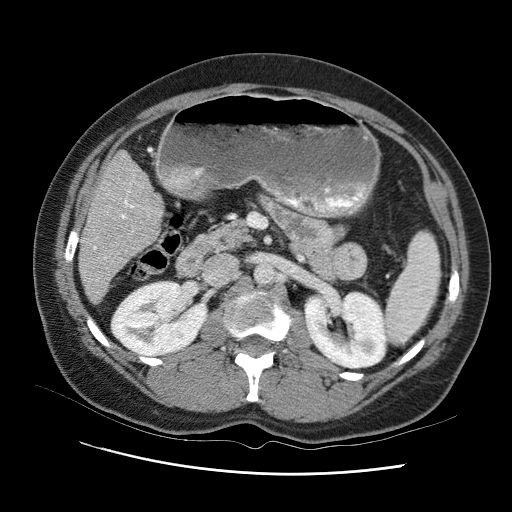
Contrast-enhanced abdominal CT (liver protocol), one axial slice. Position 36 of 95 along the scan axis. 120 kVp. One of 2 acquisitions stored at this slice position. Soft-tissue window (W 400 / L 40 HU). 512 × 512 image matrix, field of view 360 × 360 mm. Case-level facts recorded for this patient, not image findings: diagnosis: hepatocellular carcinoma (patient treated with transarterial chemoembolisation; whether this scan precedes or follows treatment is not stated here); TNM stage (as recorded): Stage-I; Child-Pugh class: B.
Structures marked on this image (semi-automatically segmented with operator editing):
- liver parenchyma outside the tumour (the mass and vessels are separate outlines, so this box may not span the whole liver): bounding box <78,144,168,312> (left, top, right, bottom; pixels)
- liver vessels: <93,204,155,275>